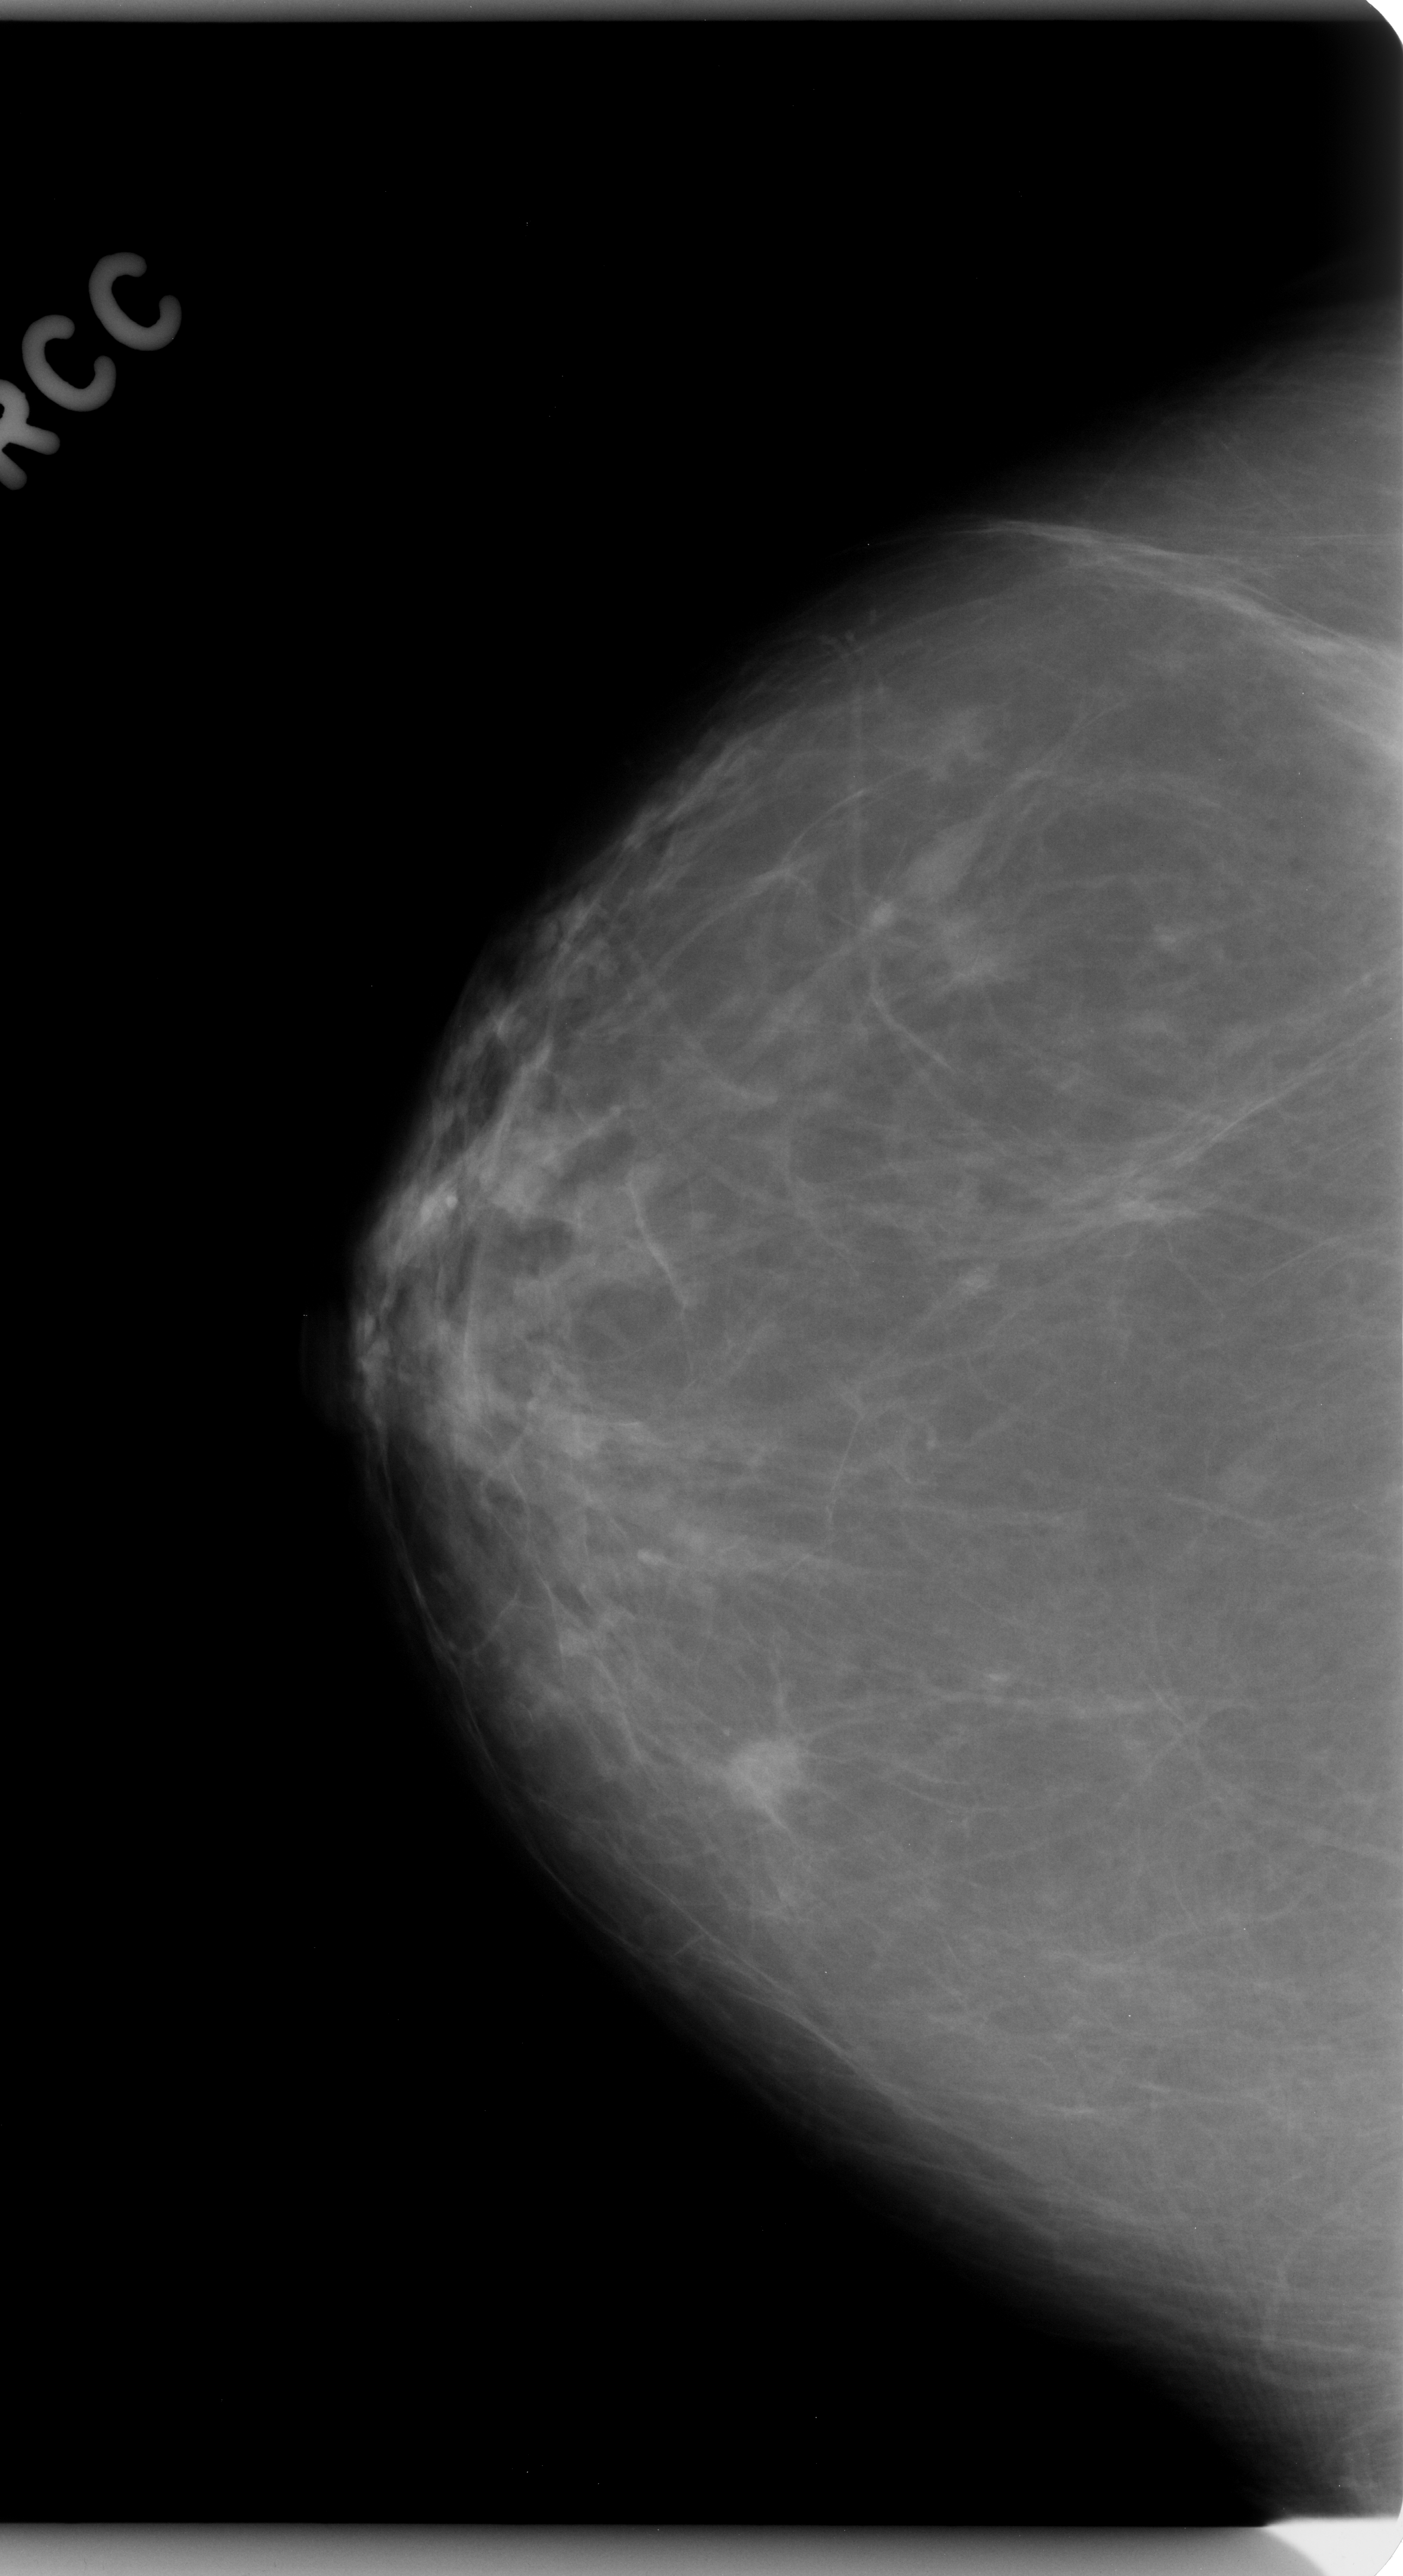
Mammogram (digitized film), right breast, craniocaudal (CC) view, breast composition: almost entirely fatty (BI-RADS density category 1 of 4).
Finding: mass, shape oval, margins spiculated; BI-RADS assessment category 5; pathology result (as recorded, not read from the image): malignant.